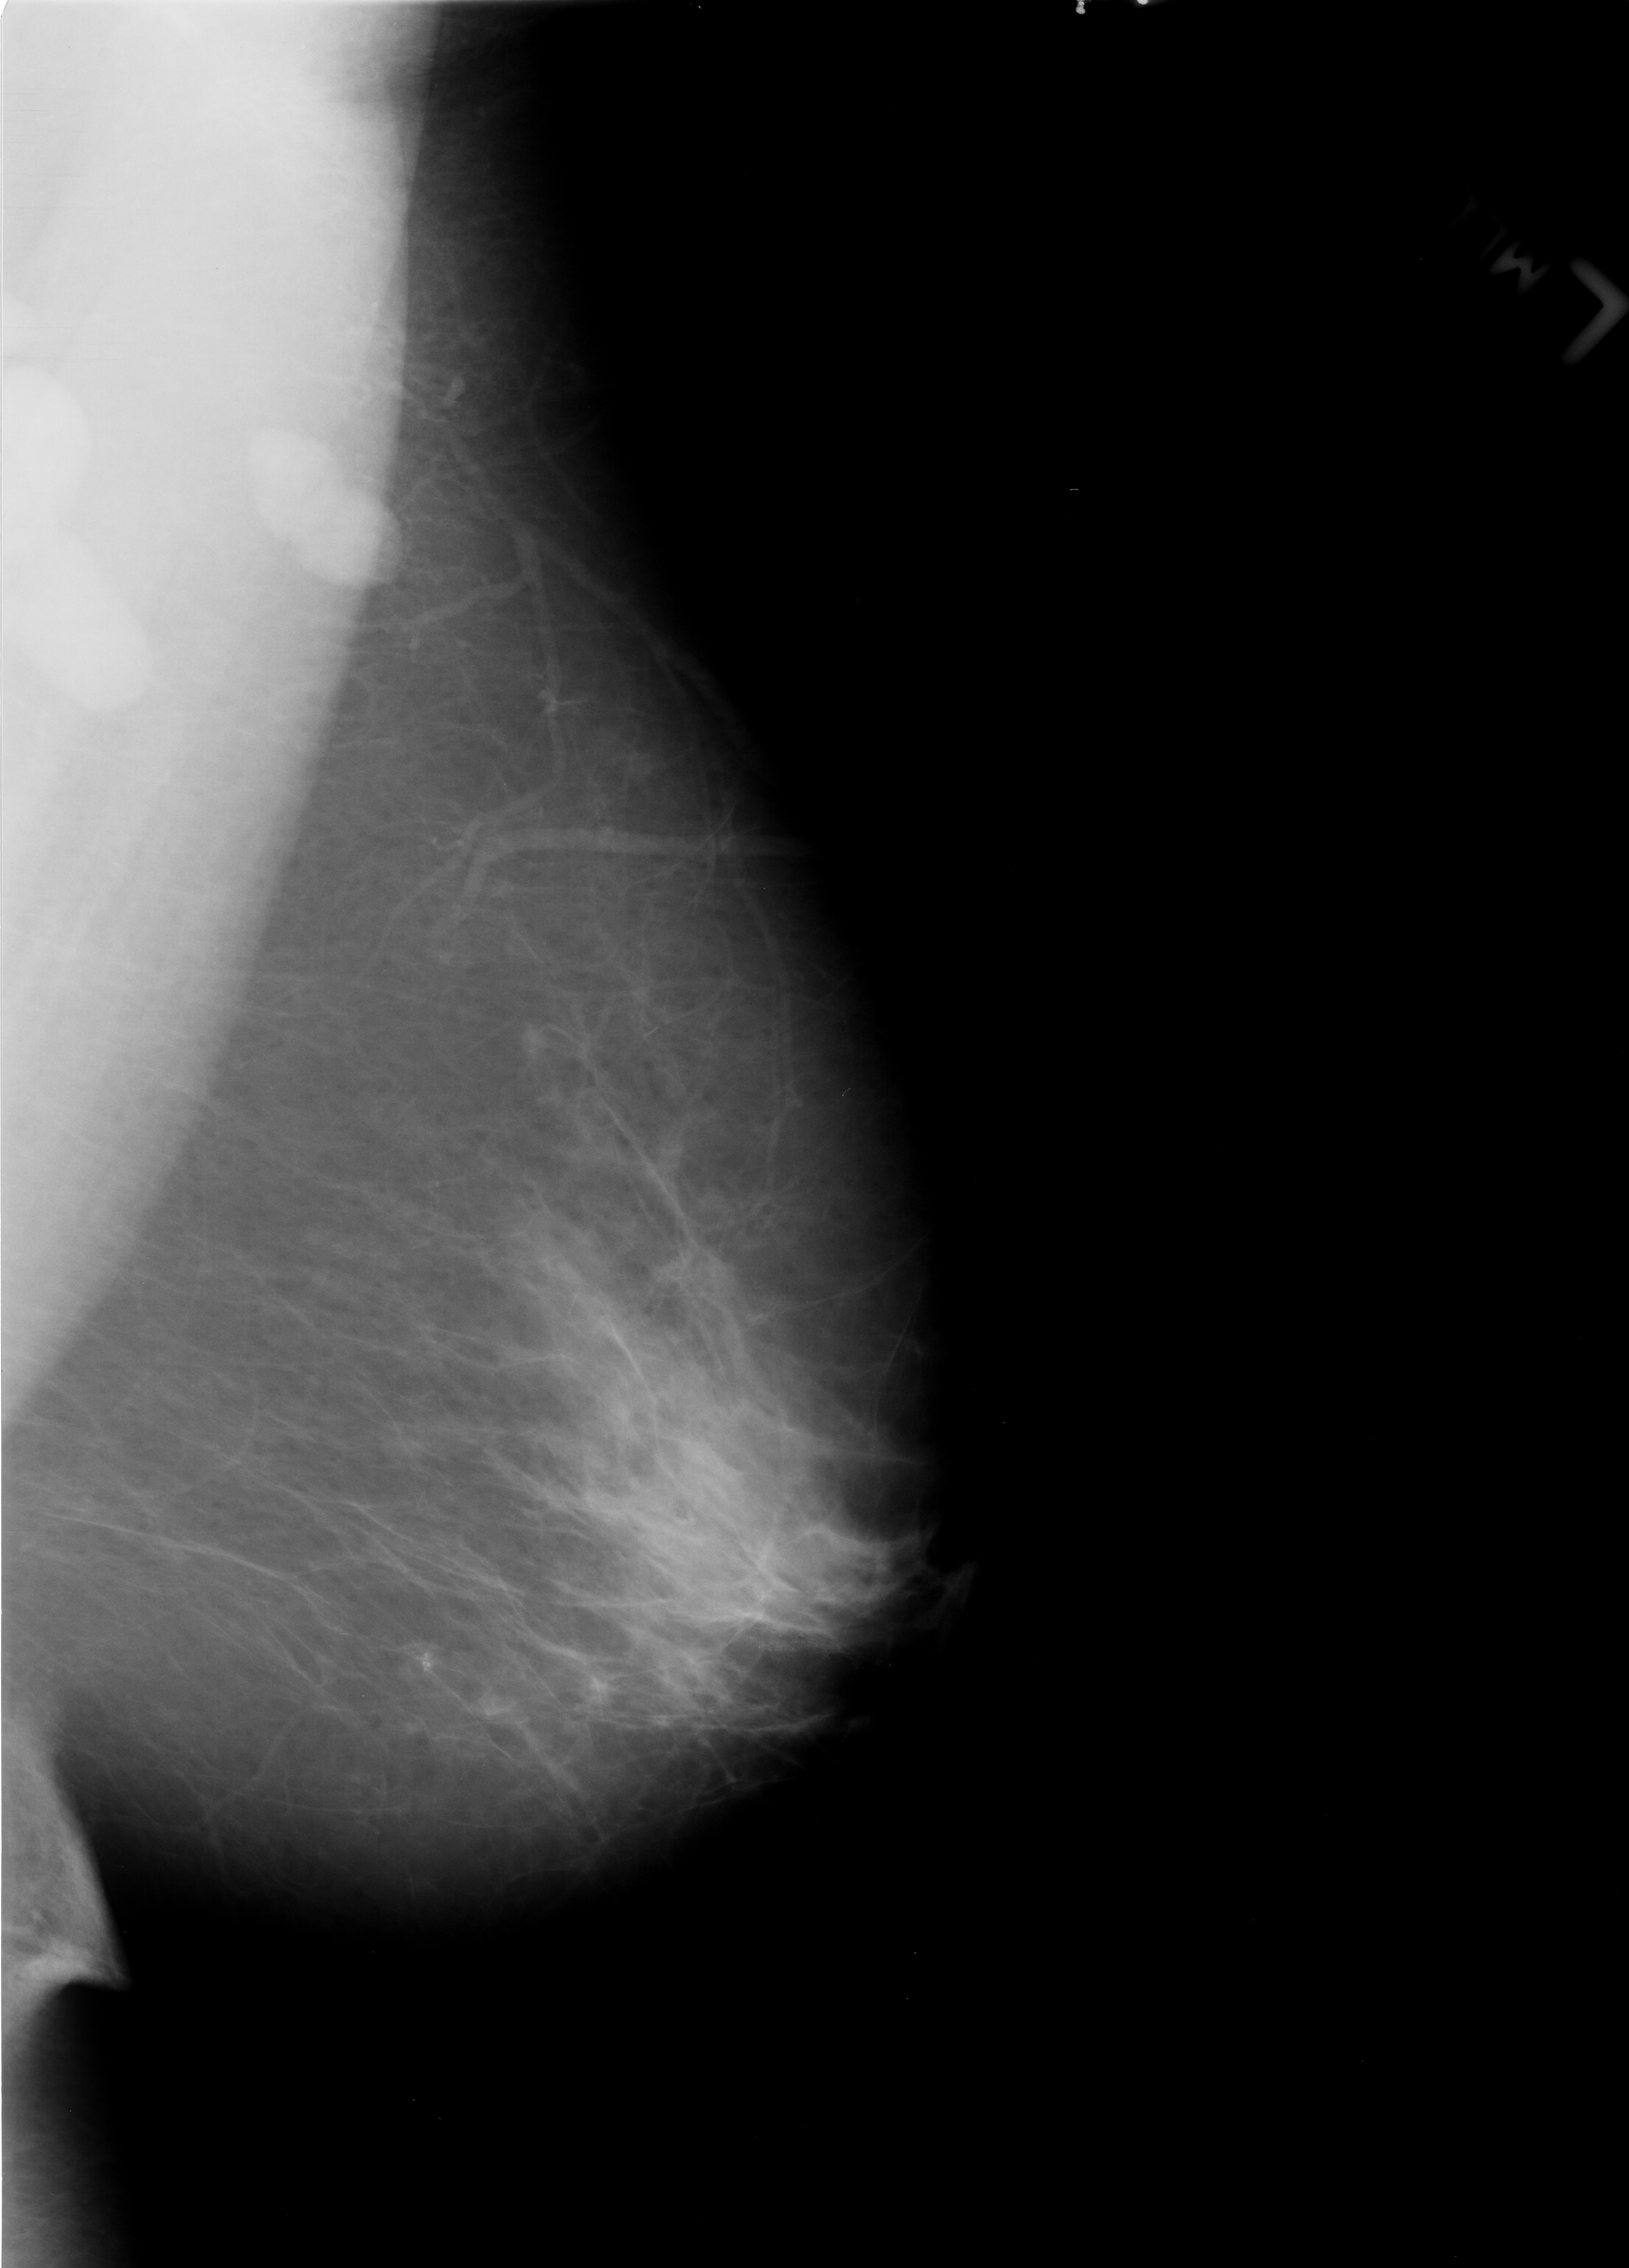
Mammogram (digitized film); left breast; mediolateral oblique (MLO) view; BI-RADS breast density category 2 (scale 1–4); 1629 × 2268 image matrix.
Marked abnormalities (boxes around the expert regions of interest):
- Finding 1 of 2: calcifications, morphology pleomorphic, distribution clustered; BI-RADS assessment category 4; subtlety rating 4 on a 1 (subtle) to 5 (obvious) scale; pathology (as recorded): benign: box from (x=373, y=1619) to (x=483, y=1715) px
- Finding 2 of 2: calcifications, morphology fine linear branching, distribution clustered / linear; BI-RADS assessment category 4; subtlety rating 2 on a 1 (subtle) to 5 (obvious) scale; pathology (as recorded): benign: (x=717, y=1612)–(x=850, y=1679)